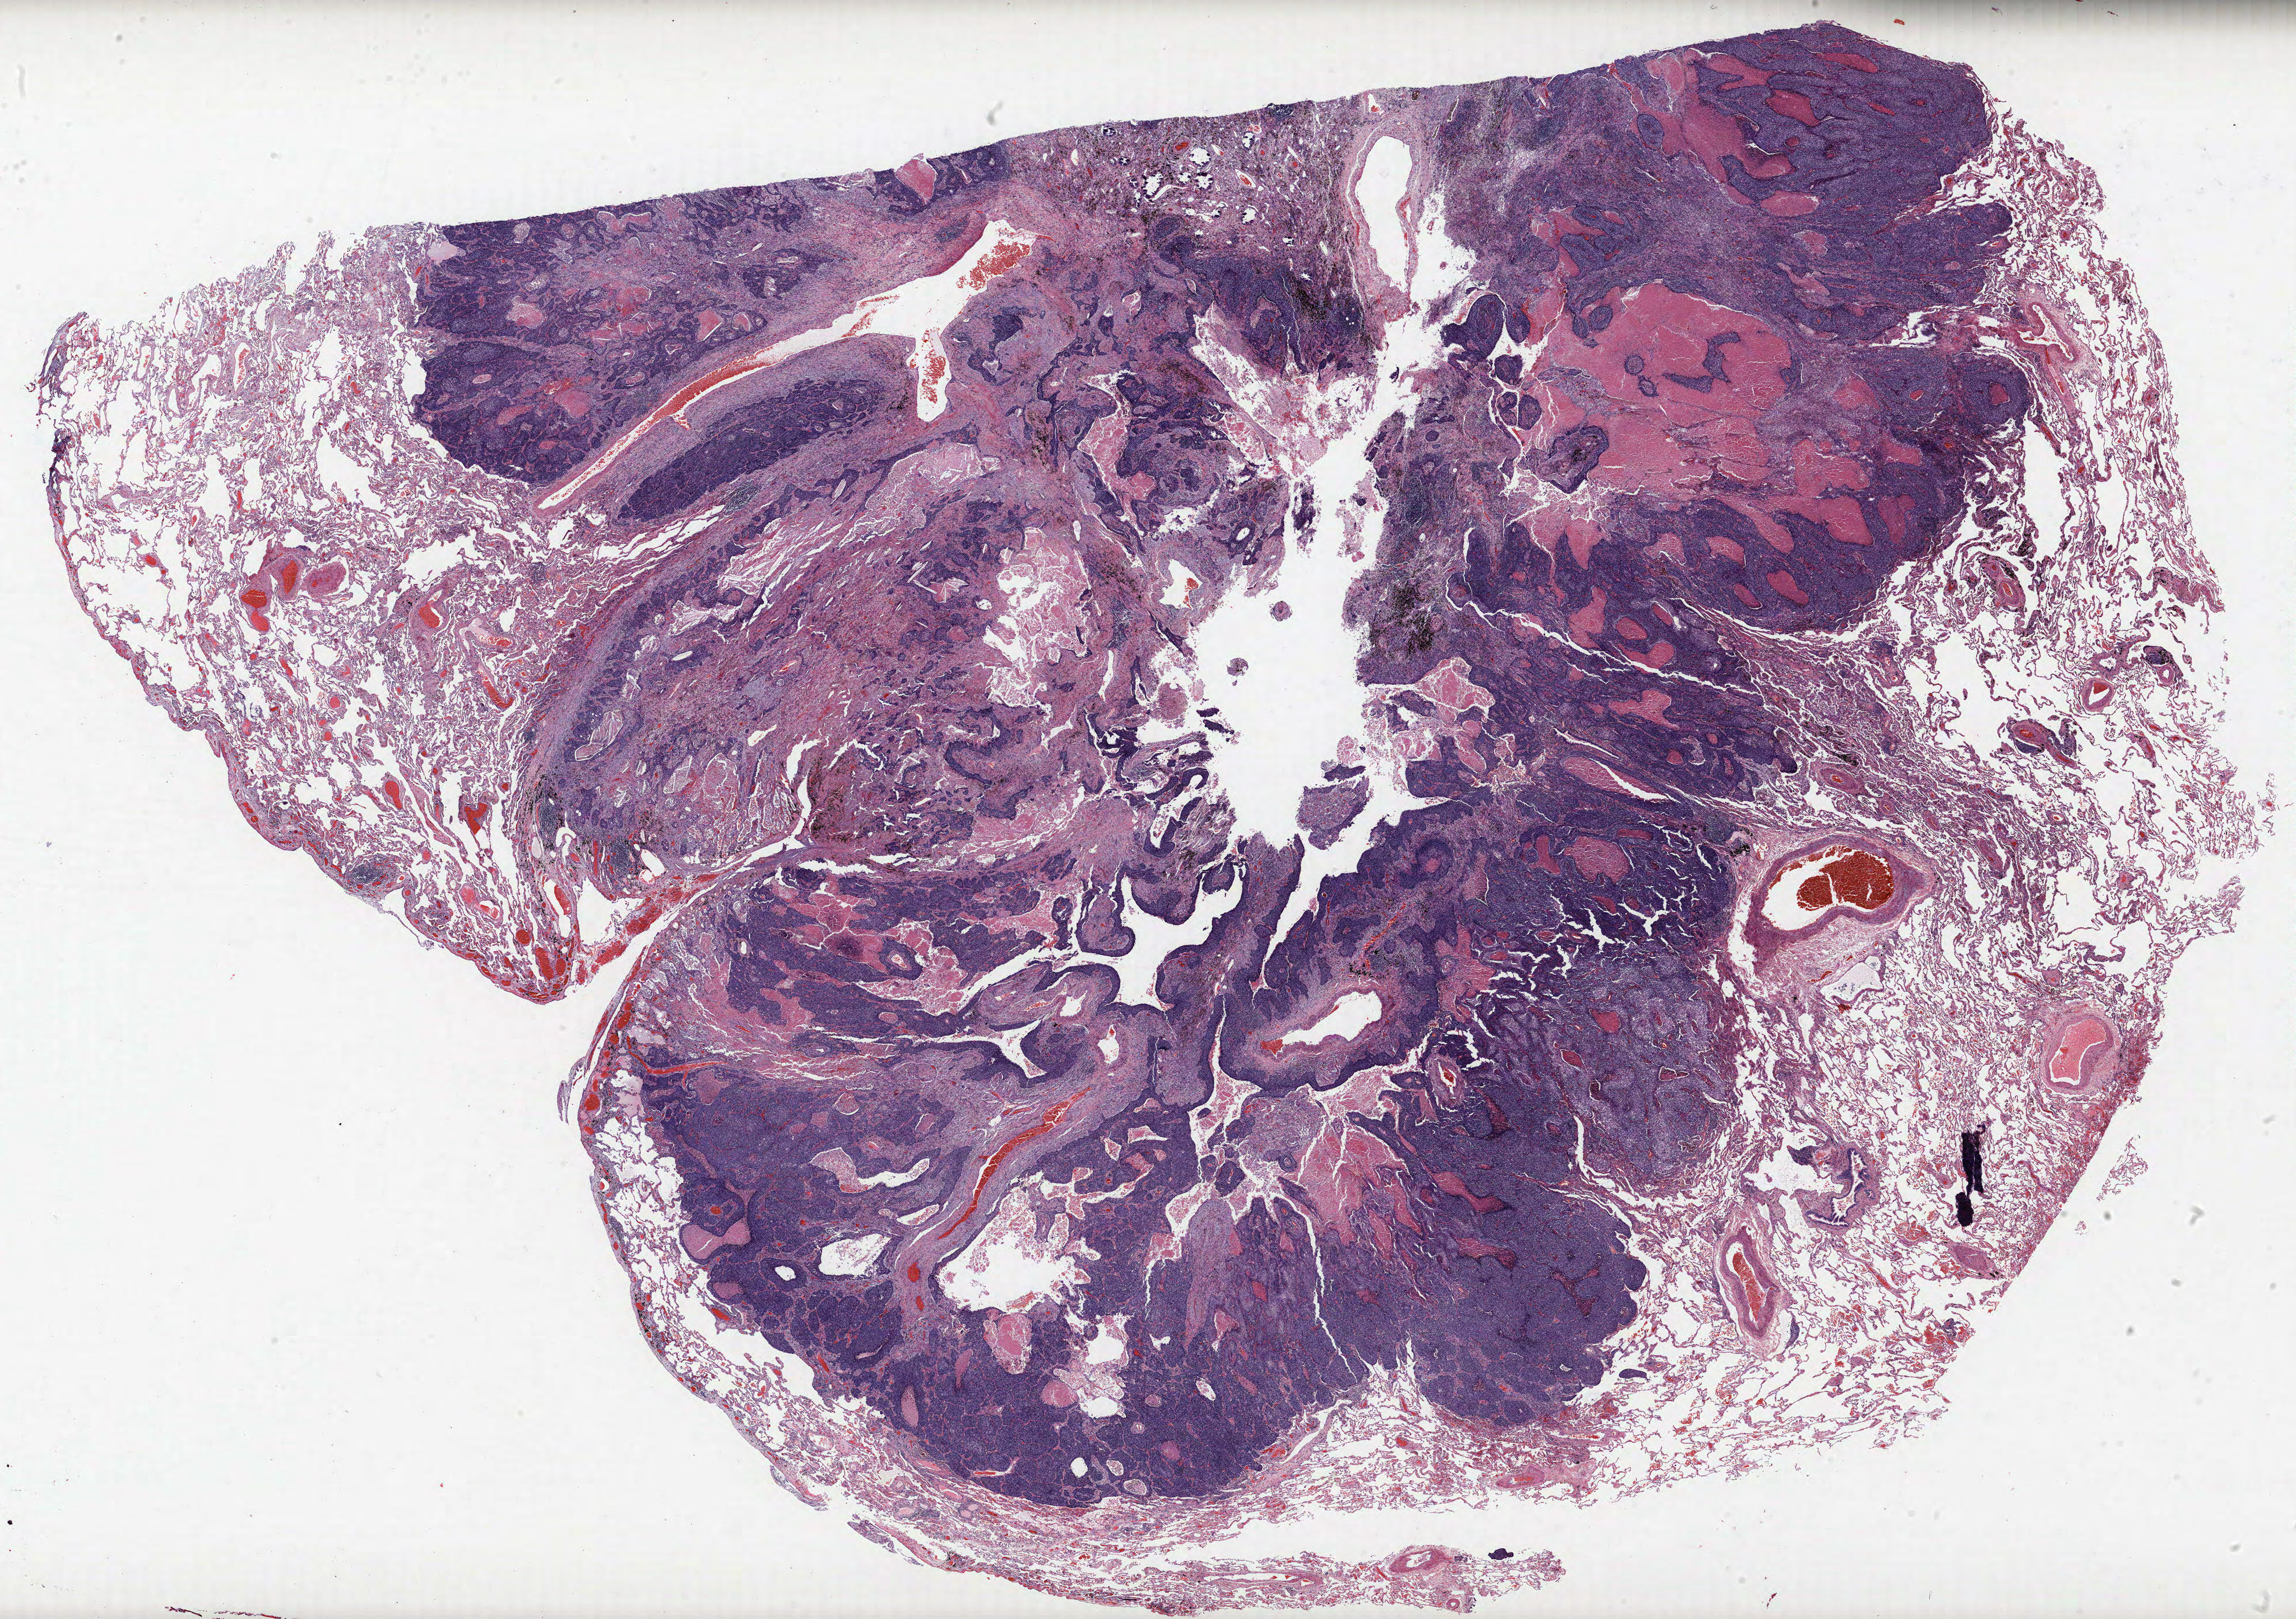
Hematoxylin and eosin (H&E) stained whole-slide image, a low-resolution overview of the entire scanned area, about 31.7 x 22.3 mm (slide scanned at 40x). FFPE section. Lung tissue. Male patient, aged 66 at enrolment. Current smoker at enrolment. Grade: poorly differentiated (G3).
- primary tumour location (clinical record): left upper lobe
- stage (AJCC 6th edition): IB
- tumour size (pathology): 30 mm
- participant's lung-cancer diagnosis: Squamous cell carcinoma, NOS (ICD-O-3 8070/3)